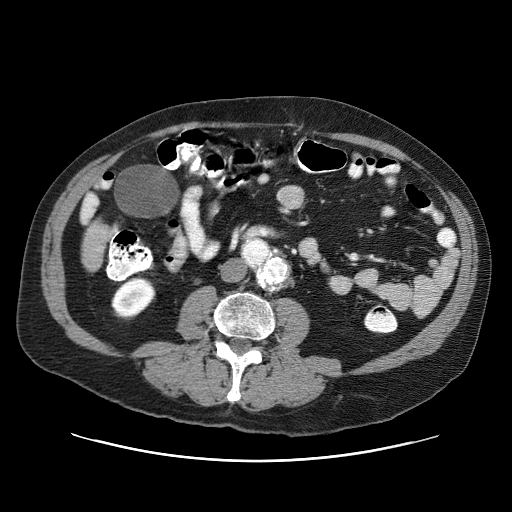
Contrast-enhanced abdominal CT (liver protocol), one axial slice. Slice 2 of 87 in the series (ordered by position). One of 3 acquisitions stored at this slice position. Soft-tissue window (W 400 / L 40 HU). 2.5 mm slice thickness. 512 × 512 image matrix. From the clinical record (not read from this slice): diagnosis: hepatocellular carcinoma (patient treated with transarterial chemoembolisation; whether this scan precedes or follows treatment is not stated here); TNM stage (as recorded): Stage-IIIA; Child-Pugh class: A; tumour size: 6 cm.
Outlined on this slice (semi-automatic segmentation, software-assisted and operator-edited):
- liver parenchyma outside the tumour (the mass and vessels are separate outlines, so this box may not span the whole liver): box from (x=80, y=192) to (x=112, y=270) px
- liver vessels: (x=83, y=195)–(x=97, y=219)